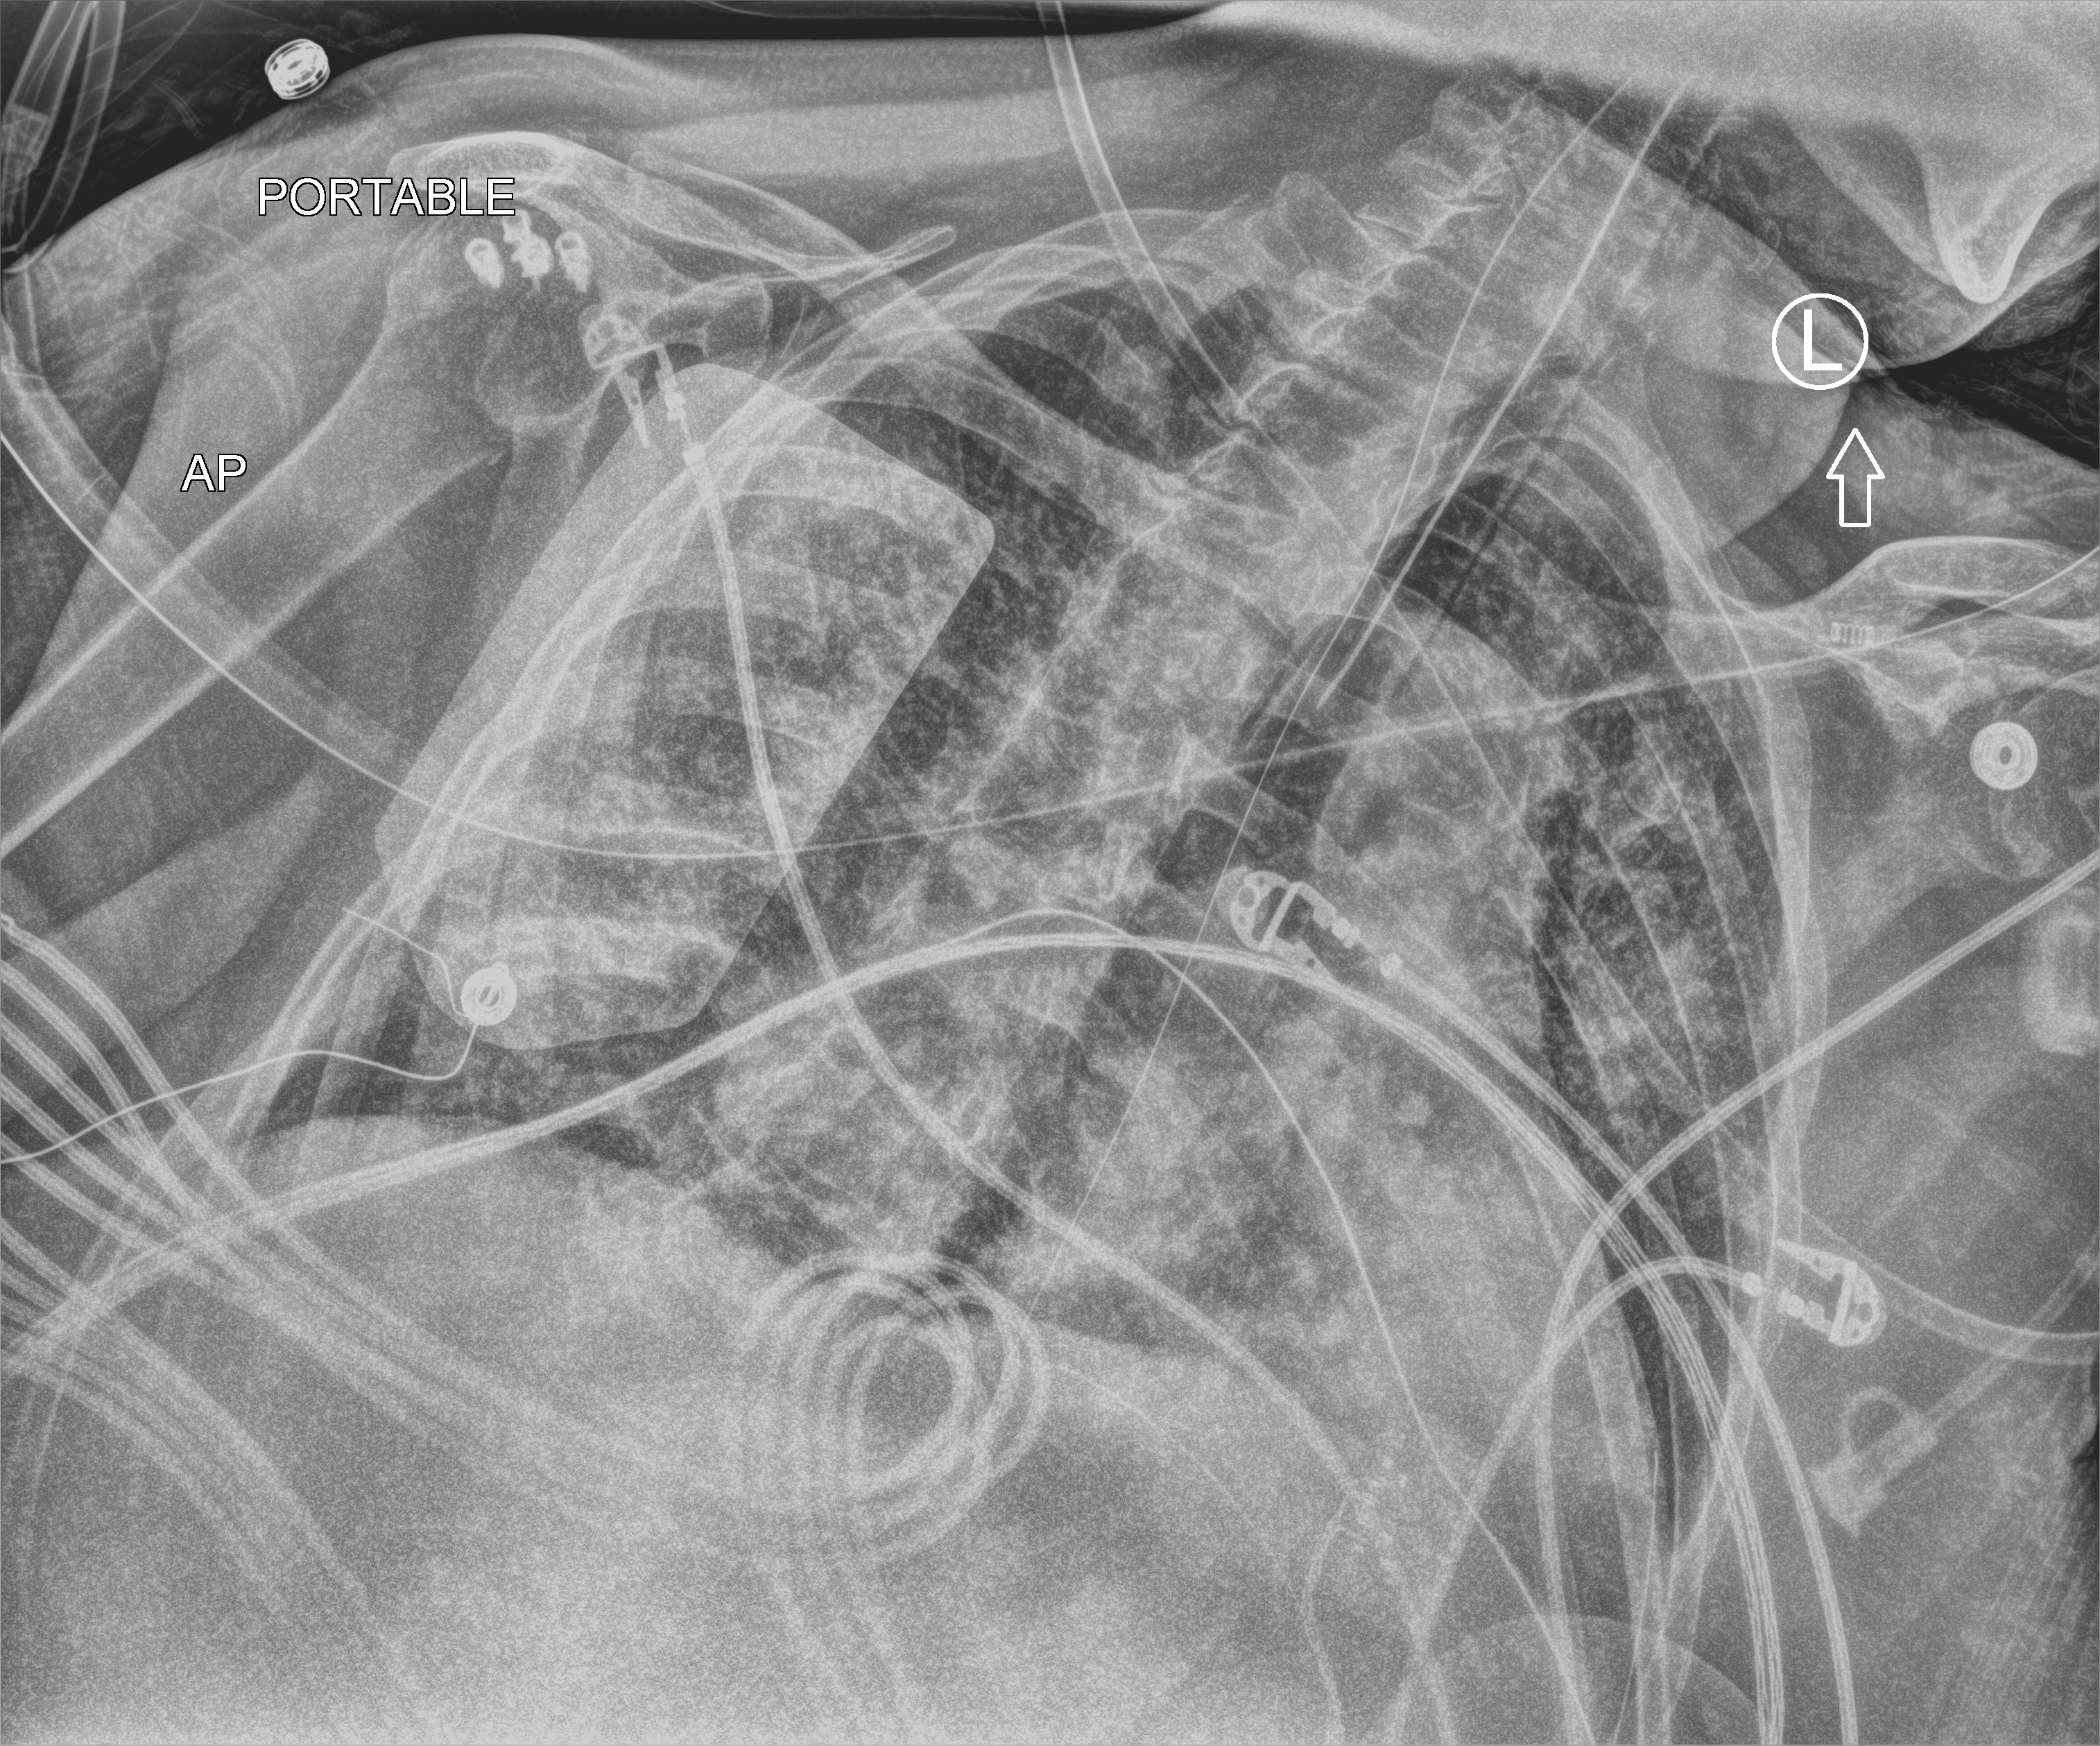
Portable chest radiograph, anteroposterior (AP) projection. Patient hospitalised with COVID-19; female, aged 60–74 years.
Hospital-stay facts (about this admission, not read from this image; timing relative to this image not recorded):
- mechanically ventilated during this hospital stay: yes
- chronic kidney disease (admission record): no